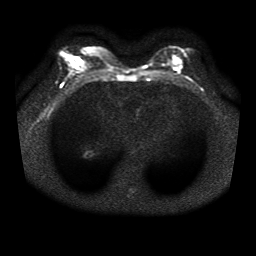
Breast MRI, one axial slice. Slice 18 of 41 in the series (ordered by position). Diffusion-weighted series; image 2 of 4 stored at this slice position (different b-values; order by instance number). 1.5 T. 5 mm slice thickness. 256 × 256 image matrix, field of view 330 × 330 mm. Female patient.
Outlined on this slice (outlined manually by an expert reader):
- tumour on diffusion-weighted imaging: box from (x=173, y=58) to (x=181, y=66) px